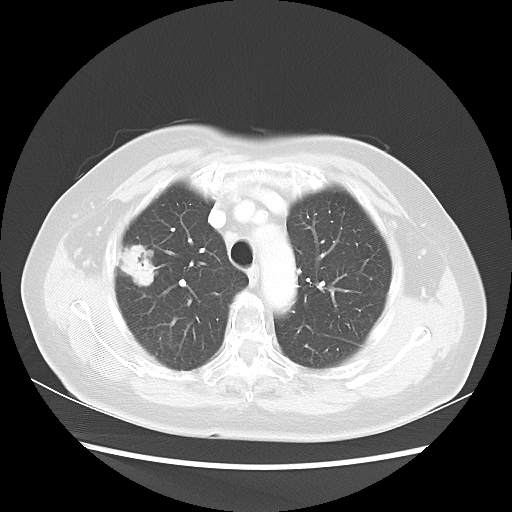
Chest CT, one axial slice. 100 kVp. Lung window (W 1500 / L -600 HU). 5 mm slice thickness. 512 × 512 image matrix, field of view 360 × 360 mm. Female patient, age 75 years. From the clinical record (not read from this slice): clinical TNM (as recorded): T1c N0 M0.
Structures marked on this image (bounding box drawn by a radiologist):
- lung tumour (recorded histology: adenocarcinoma): bounding box [x1, y1, x2, y2] px = [116, 238, 158, 290]